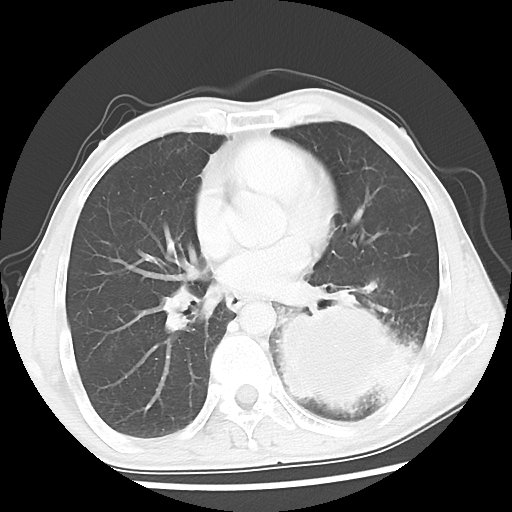
Chest CT, one axial slice; position 23 of 52 along the scan axis; lung window (W 1500 / L -600 HU); 512 × 512 image matrix. Patient: male, 60 years. Case-level facts recorded for this patient, not image findings: clinical TNM (as recorded): T4 N0 M0.
Structures marked on this image (rectangle marked by the reading radiologist):
- lung tumour (recorded histology: squamous cell carcinoma): bounding box (x1, y1, x2, y2) in pixels: (265, 294, 425, 431)